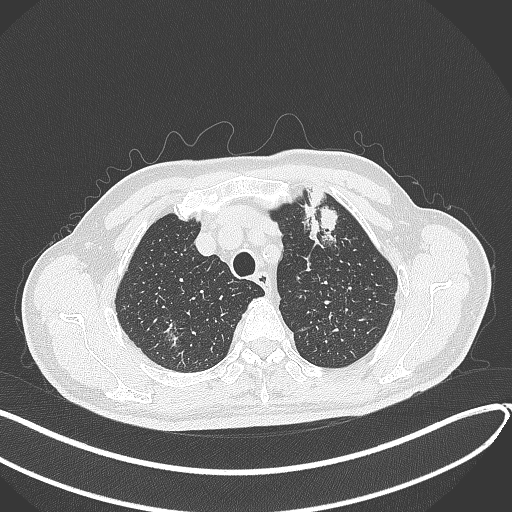
Chest CT, one axial slice; slice 348 of 459 in the series (ordered by position); lung window (W 1500 / L -600 HU); 1 mm slice thickness; 512 × 512 image matrix, field of view 400 × 400 mm. Patient: male, 74 years. Case-level facts recorded for this patient, not image findings: clinical TNM (as recorded): T2b N0 M1c.
Structures marked on this image (bounding box drawn by a radiologist):
- lung tumour (recorded histology: adenocarcinoma): bounding box [x1, y1, x2, y2] px = [299, 182, 345, 252]